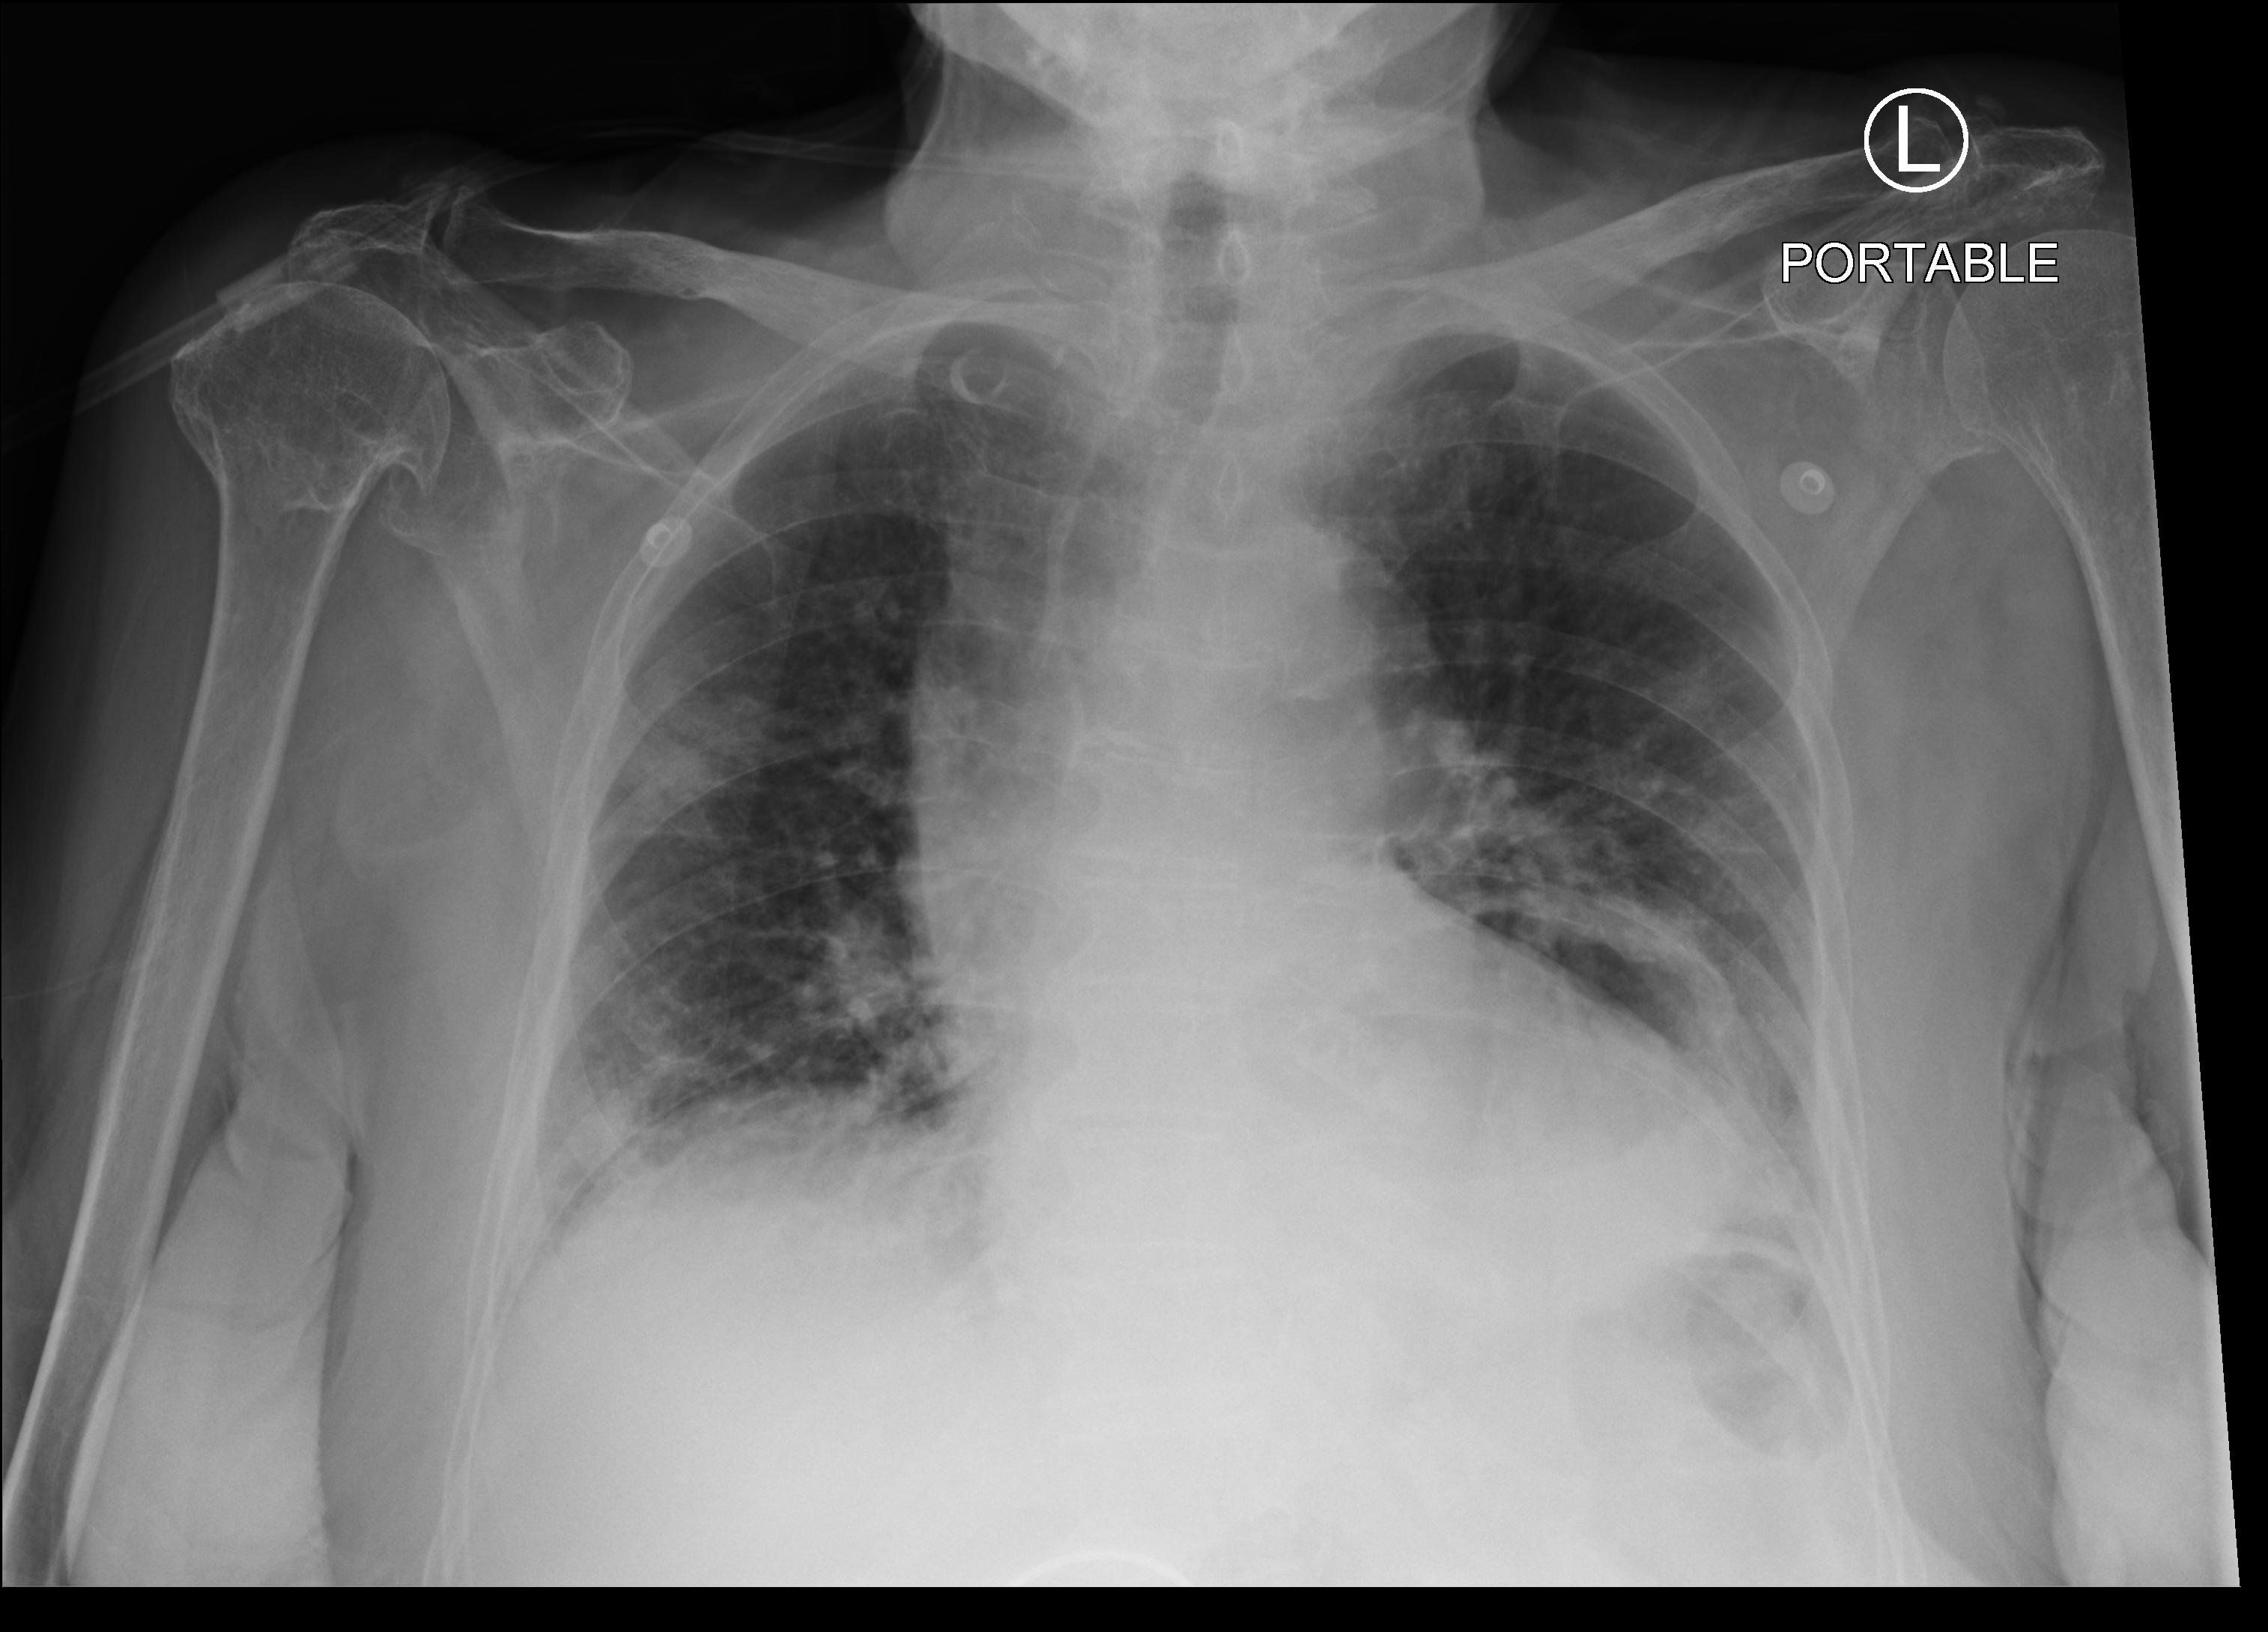
Bedside chest radiograph (computed radiography), anteroposterior (AP) projection. Female patient hospitalised with COVID-19, age 75–90 years.
From the hospital-stay record, not from the radiograph (when in the stay this image was taken is not recorded): hypertension (admission record): yes; length of hospital stay: 9 days.